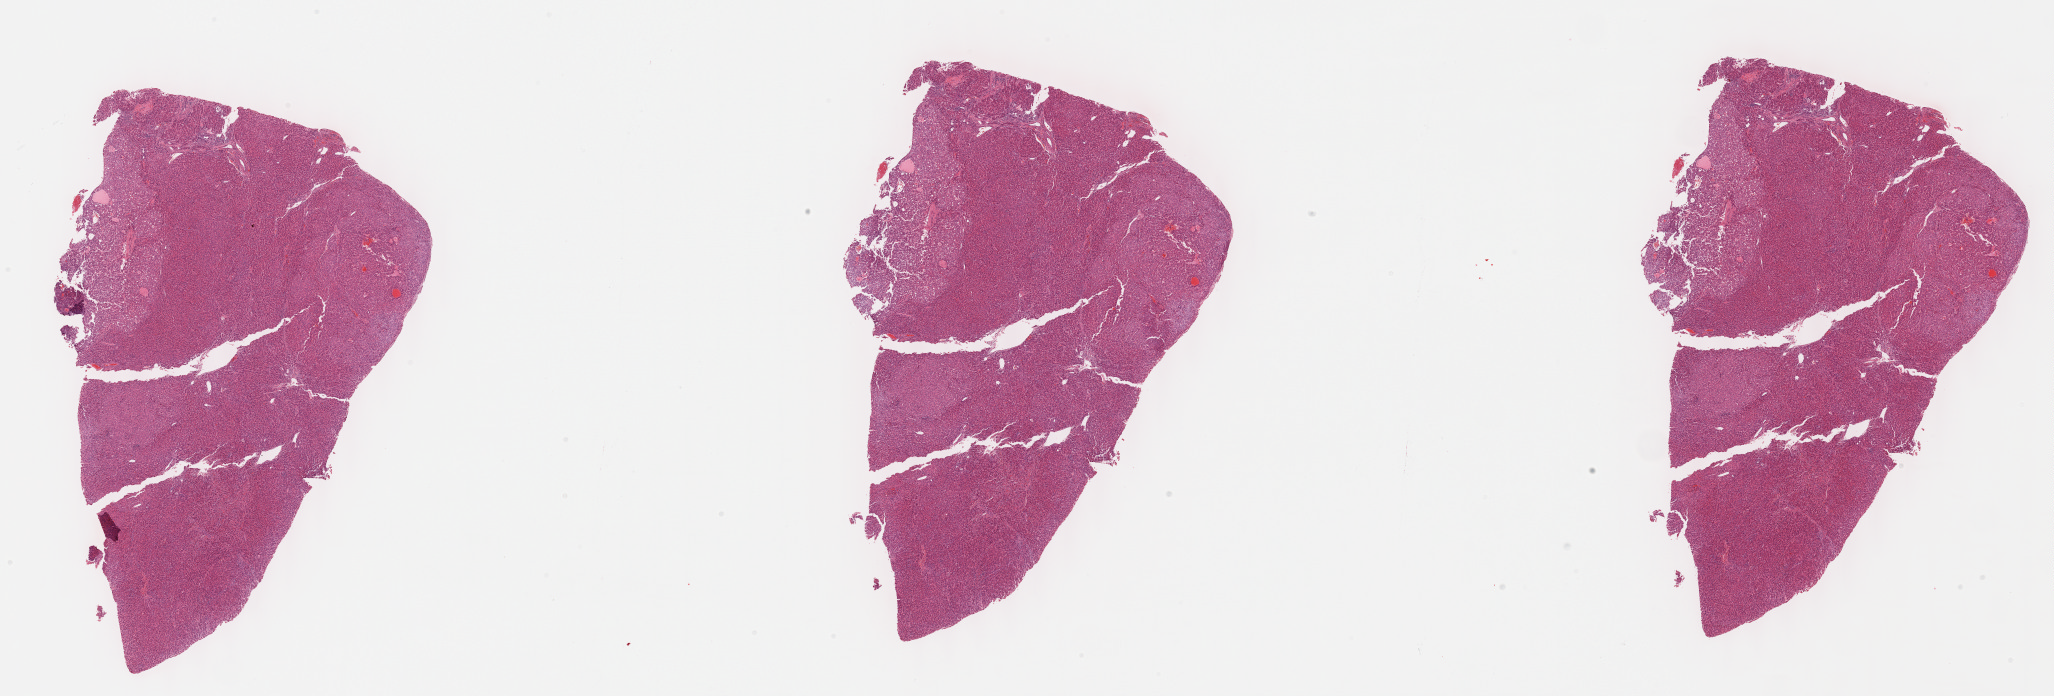
Hematoxylin and eosin (H&E) stained whole-slide image, low-resolution overview of the scanned area, about 33.2 x 11.2 mm, formalin-fixed paraffin-embedded (FFPE) diagnostic section, primary tumour sample from the liver. Male, age 40 years at initial diagnosis. Histologic grade: G3 (poorly differentiated).
• diagnosis: Hepatocellular carcinoma, NOS
• AJCC pathologic stage: I (6th edition)